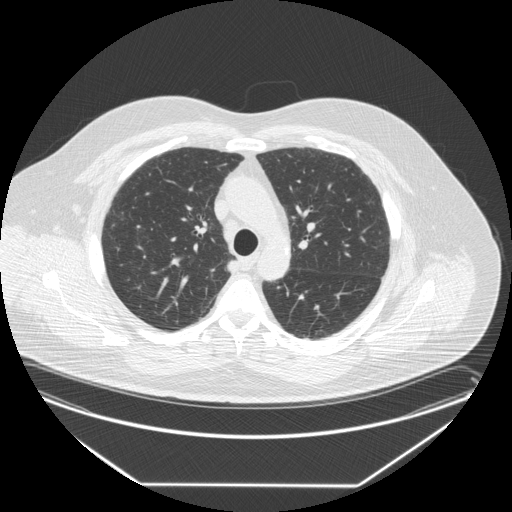
Low-dose screening chest CT, one axial slice; slice 193 of 258 in the series (ordered by position); 120 kVp; lung window (W 1500 / L -600 HU); 512 × 512 image matrix.
Structures marked on this image (outlined manually by an expert reader):
- lesion 1 (tumor, upper lobe of right lung): bounding box <227,260,239,273> (left, top, right, bottom; pixels)